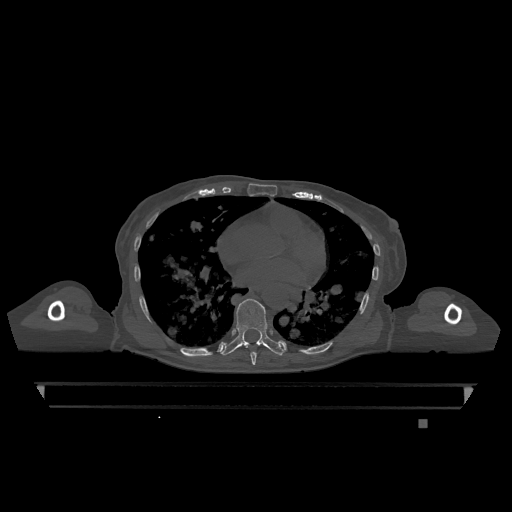
CT including the spine, one axial slice; position 703 of 1317 along the scan axis; bone window (W 1800 / L 400 HU); 0.5 mm slice thickness; 512 × 512 image matrix, field of view 500 × 500 mm. Patient: female, 74 years. From the clinical record (not read from this slice): primary cancer: lung.
Structures marked on this image (semi-automatically segmented with operator editing):
- T7 vertebra: bounding box [x1, y1, x2, y2] px = [250, 352, 257, 365]
- T9 vertebra: [221, 298, 284, 356]